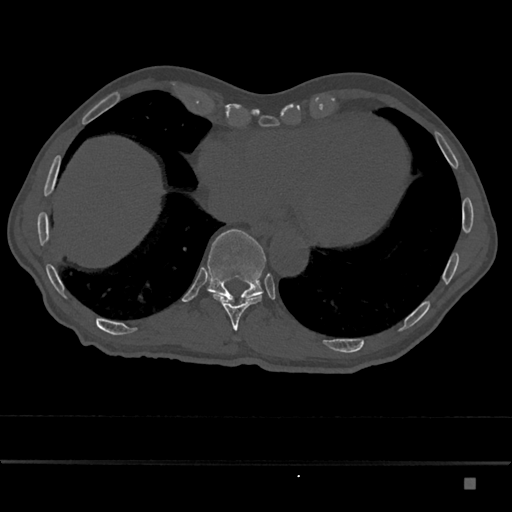
CT including the spine, one axial slice; 120 kVp; bone window (W 1800 / L 400 HU); 512 × 512 image matrix. Patient: male, 72 years. From the clinical record (not read from this slice): primary cancer: prostate.
Structures marked on this image (semi-automatically segmented with operator editing):
- T10 vertebra: box from (x=213, y=294) to (x=262, y=331) px
- T11 vertebra: (x=207, y=229)–(x=266, y=302)